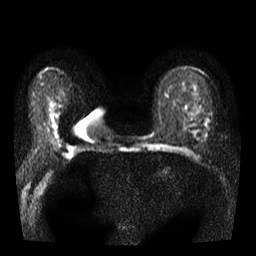
Breast MRI, one axial slice; position 21 of 38 along the scan axis; diffusion-weighted series; image 2 of 4 stored at this slice position (different b-values; order by instance number); 3 T; 256 × 256 image matrix. Female patient.
Structures marked on this image (manually delineated by an expert):
- tumour on diffusion-weighted imaging: bounding box (x1, y1, x2, y2) in pixels: (207, 121, 209, 123)